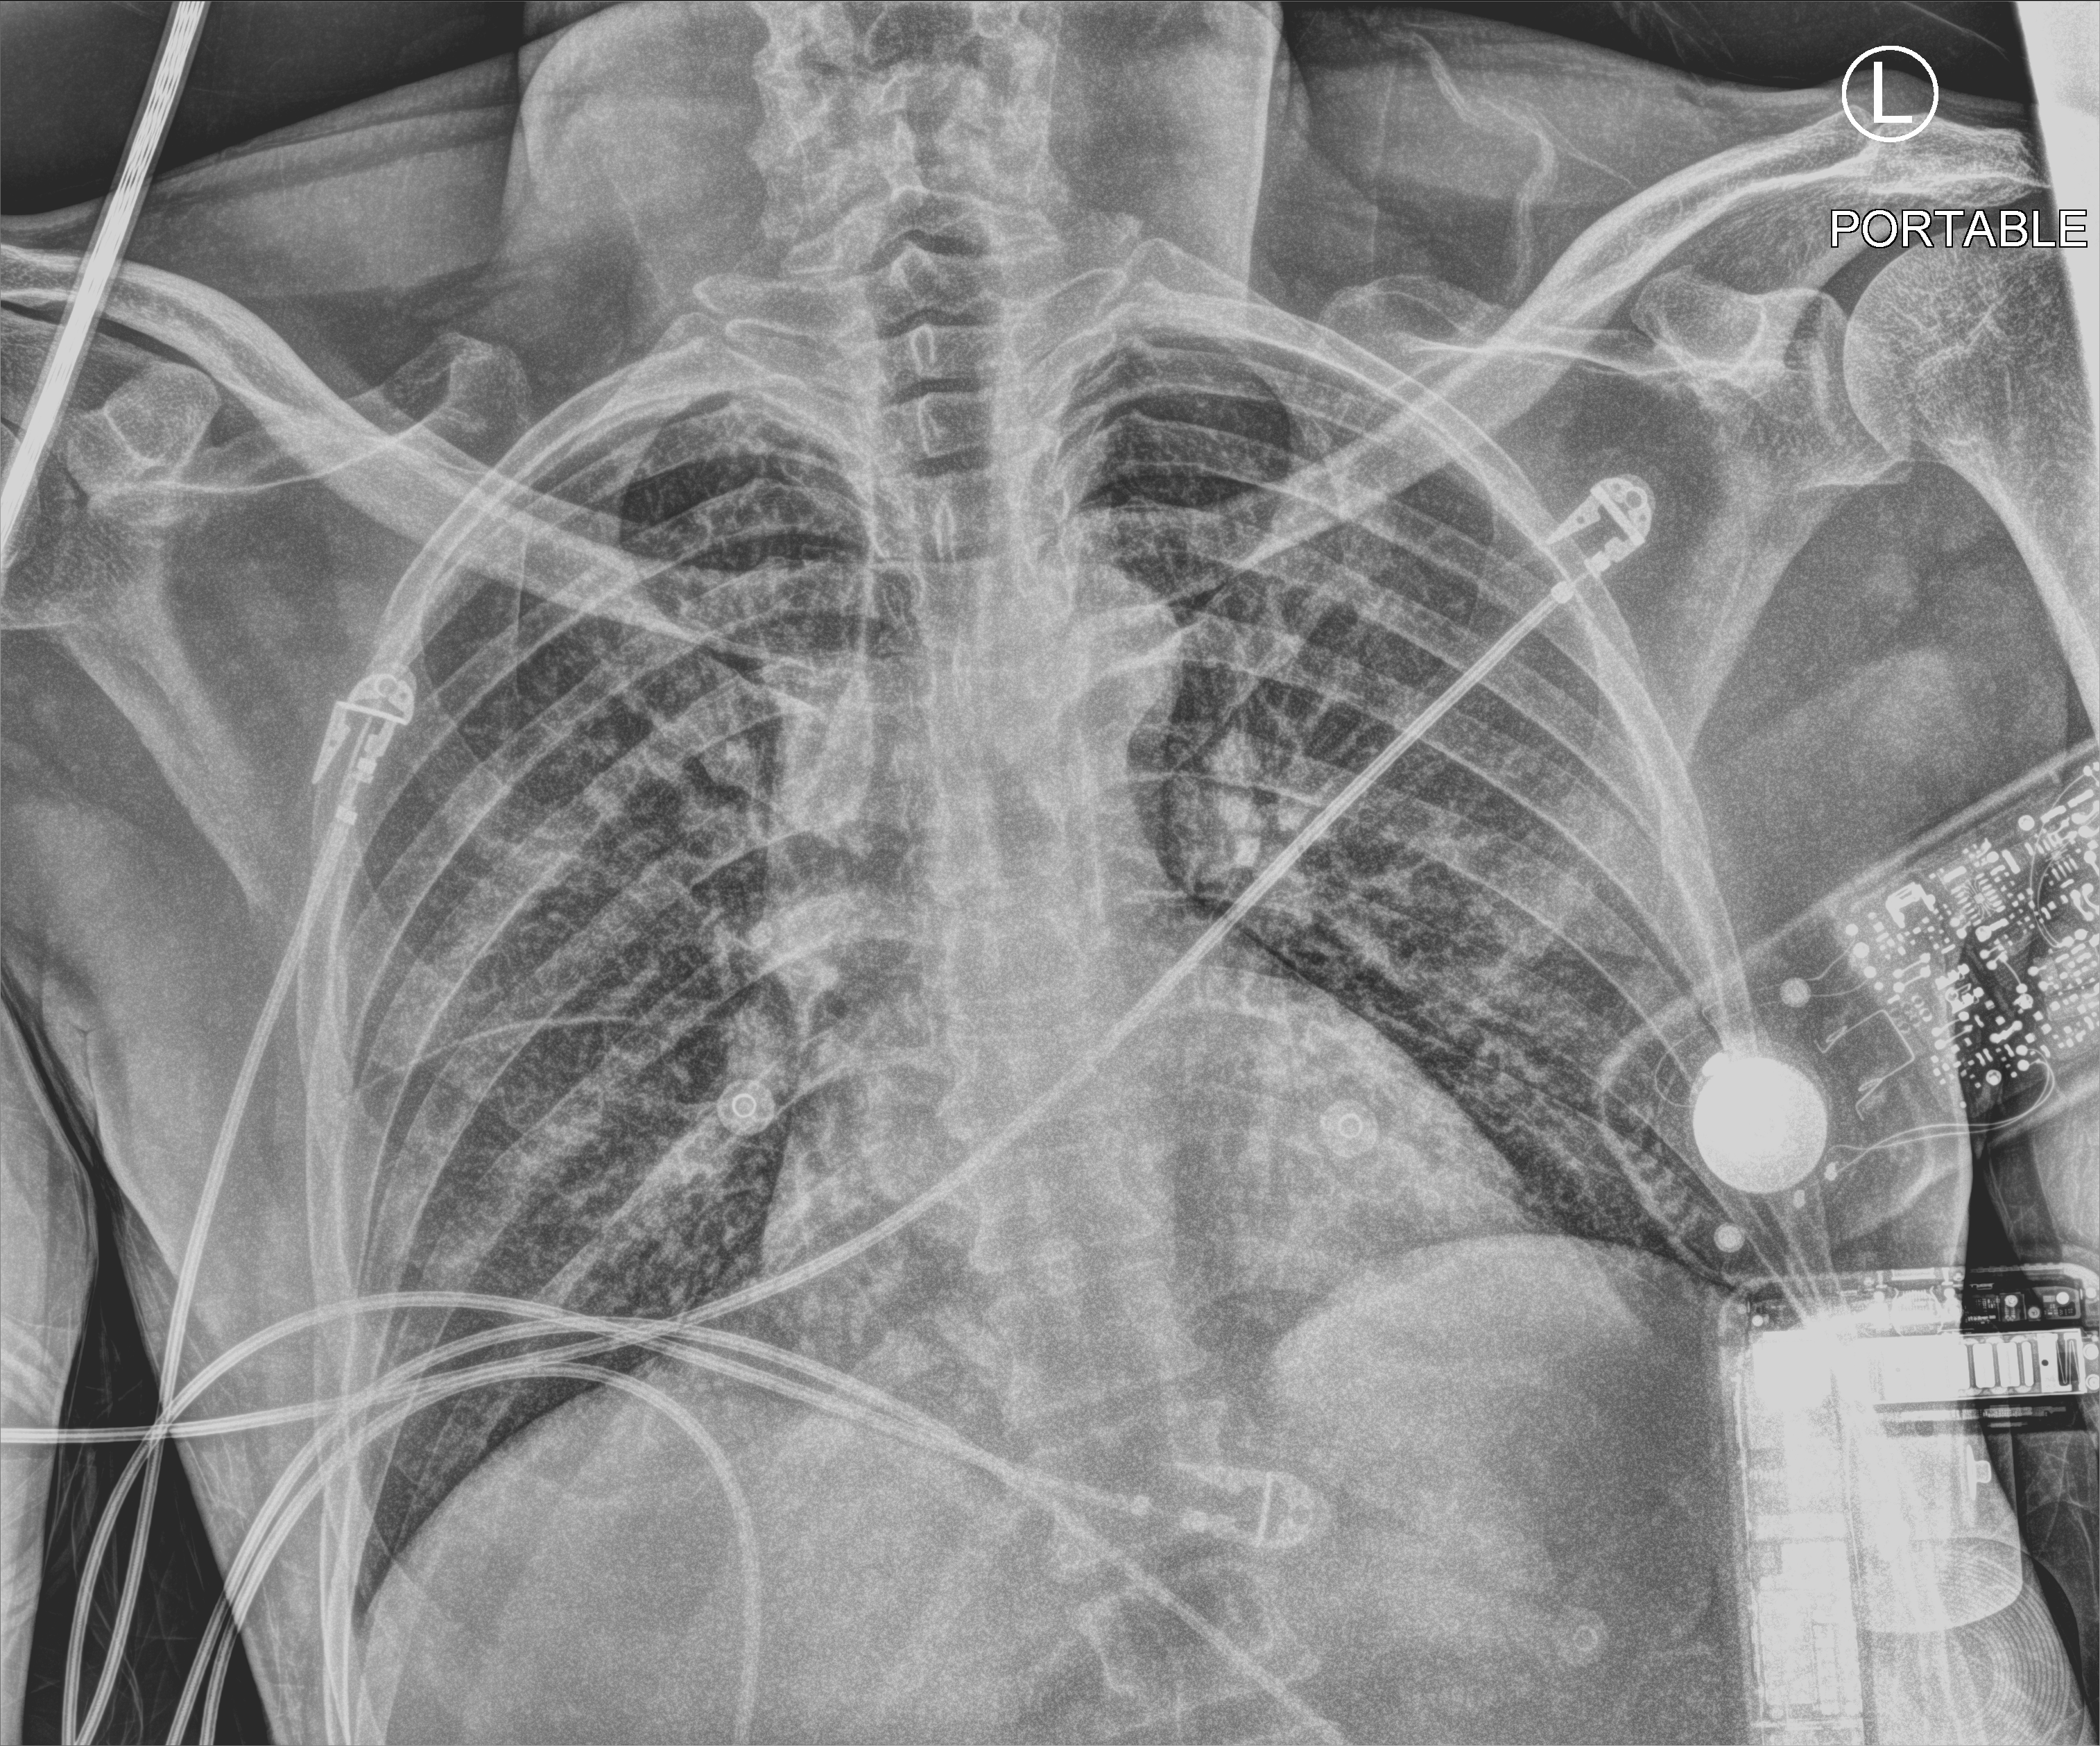
Bedside chest radiograph (computed radiography), anteroposterior (AP) projection. Patient hospitalised with COVID-19; male, aged 18–59 years.
Admission-level facts for this patient (not findings on this image; timing relative to this image not recorded):
- admitted to intensive care during this hospital stay: yes
- mechanically ventilated during this hospital stay: yes